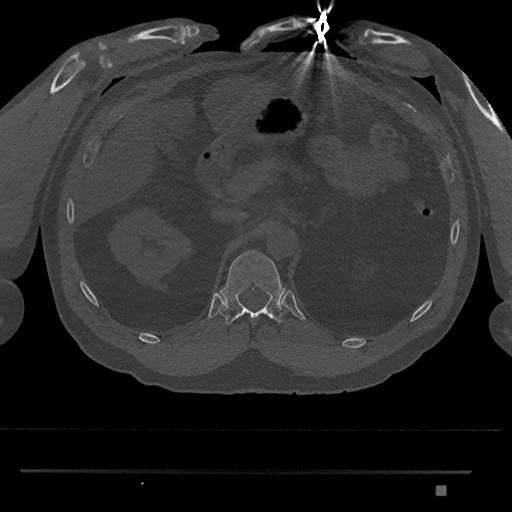
CT including the spine, one axial slice. Position 892 of 1134 along the scan axis. Reconstruction kernel Br40s/3. 120 kVp. Bone window (W 1800 / L 400 HU). 0.5 mm slice thickness. 512 × 512 image matrix, field of view 429 × 429 mm. Male patient, age 65 years. Case-level facts recorded for this patient, not image findings: primary cancer: prostate.
Structures marked on this image (semi-automatically segmented with operator editing):
- T12 vertebra: bounding box (x1, y1, x2, y2) in pixels: (219, 250, 288, 325)